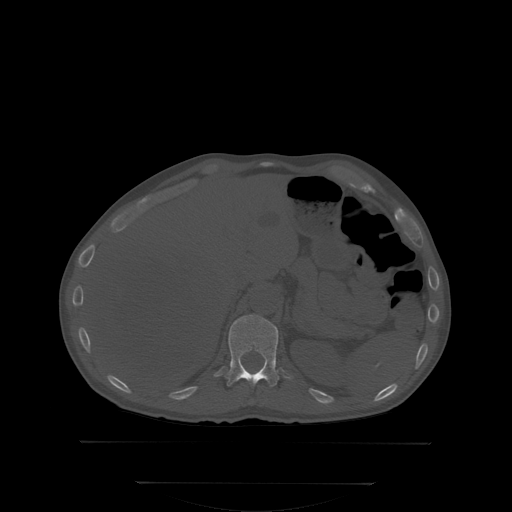
CT including the spine, one axial slice. Position 169 of 350 along the scan axis. Bone window (W 1800 / L 400 HU). 512 × 512 image matrix, field of view 500 × 500 mm. Male patient, age 58 years. From the clinical record (not read from this slice): primary cancer: prostate; vertebrae with lytic lesions (as recorded): L1.
Outlined on this slice (semi-automatic segmentation, software-assisted and operator-edited):
- T12 vertebra: box from (x=226, y=314) to (x=279, y=388) px